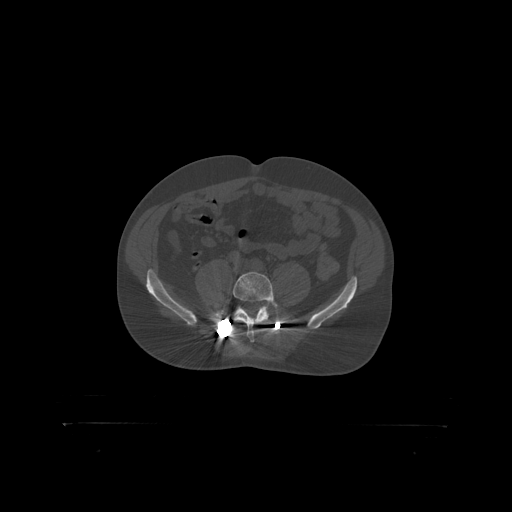
CT including the spine, one axial slice. Position 204 of 399 along the scan axis. Bone window (W 1800 / L 400 HU). 512 × 512 image matrix, field of view 650 × 650 mm. Patient: male, 46 years. Case-level facts recorded for this patient, not image findings: primary cancer: skin.
Annotated regions visible in this slice (semi-automatically segmented with operator editing):
- L5 vertebra: bounding box (x1, y1, x2, y2) in pixels: (233, 272, 278, 319)